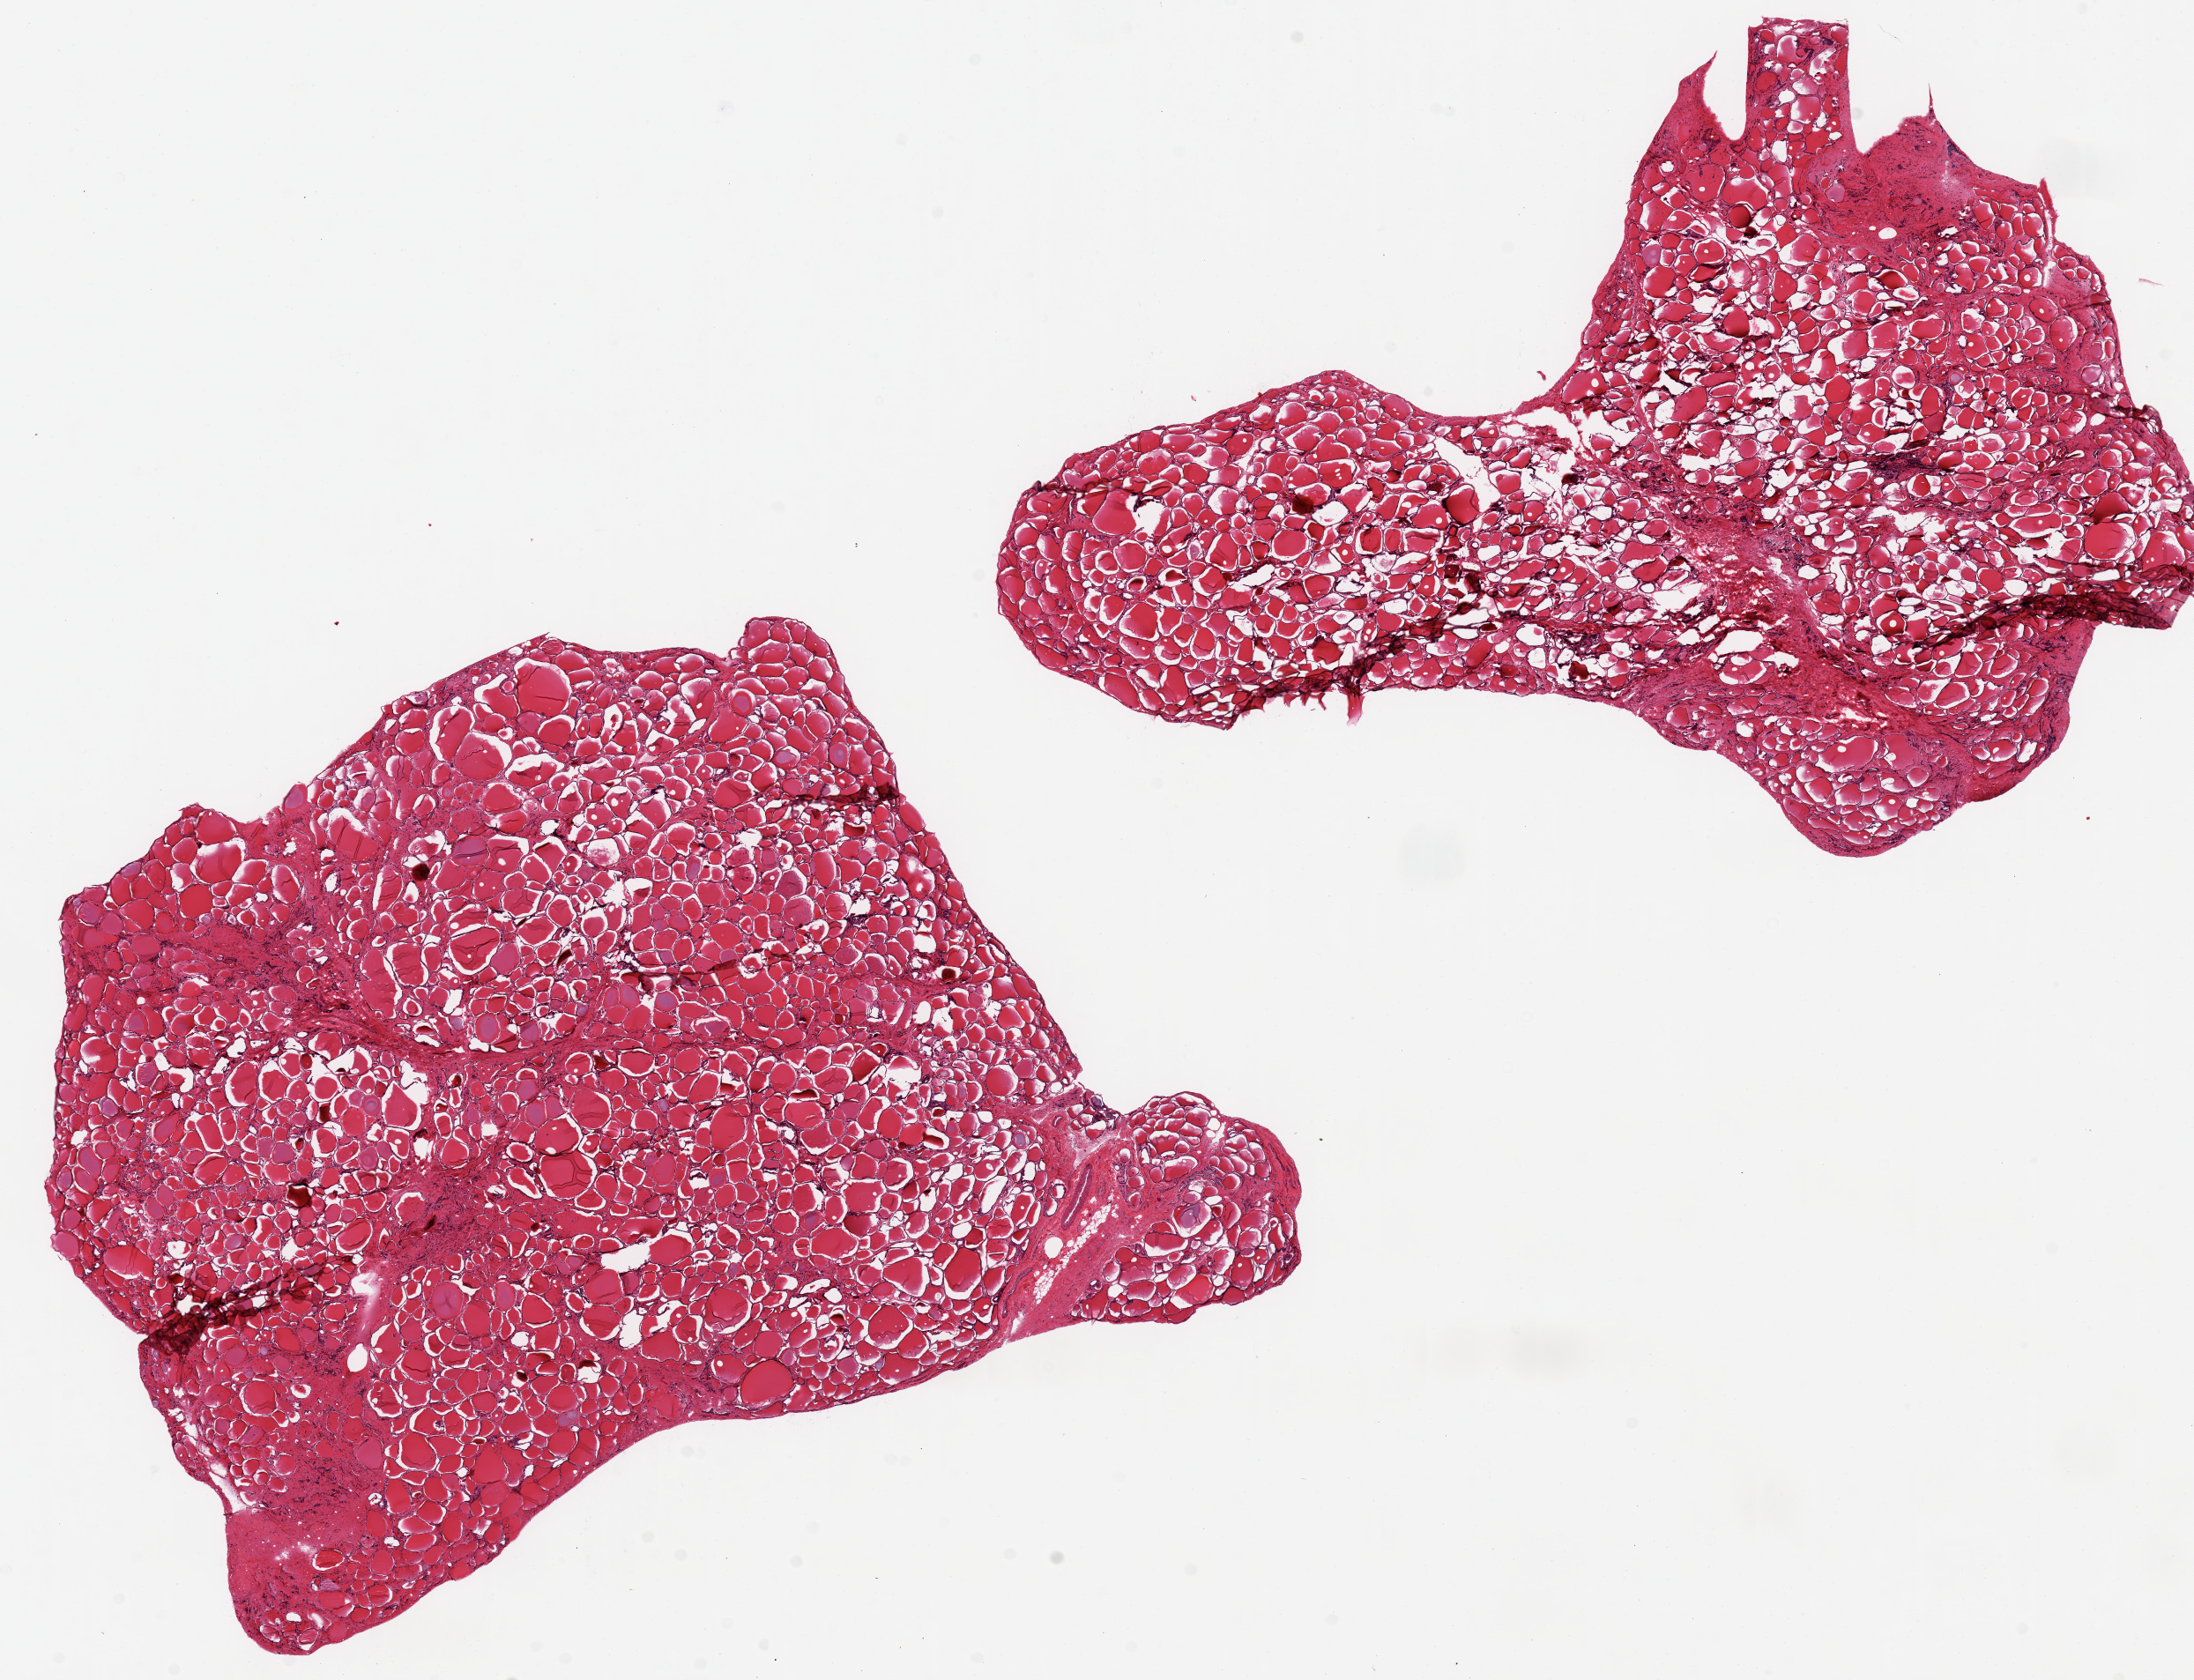
Digitized H&E-stained section, brightfield, low-resolution overview of the scanned area, about 19.7 x 15.1 mm (from a 20x scan). PAXgene-fixed, paraffin-embedded tissue. Section of thyroid (target tissue). Tissue donor sample. Male donor.
* review note (as recorded): 2 pieces, 10x8 & 10x7mm